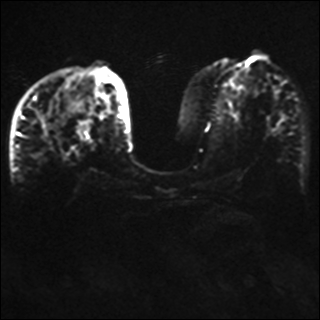
Breast MRI, one axial slice. Slice 16 of 42 in the series (ordered by position). Diffusion-weighted series; image 2 of 4 stored at this slice position (different b-values; order by instance number). 1.5 T. 320 × 320 image matrix, field of view 330 × 330 mm. Female patient.
Annotated regions visible in this slice (manually delineated by an expert):
- tumour on diffusion-weighted imaging: bounding box <40,115,45,132> (left, top, right, bottom; pixels)